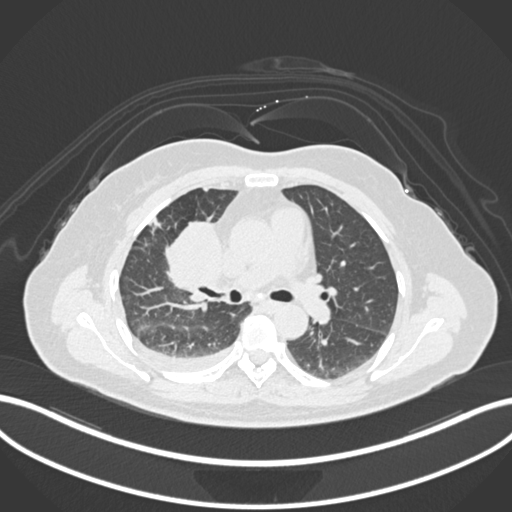
Chest CT, one axial slice. Slice 86 of 172 in the series (ordered by position). Reconstruction kernel B30f. 120 kVp. Lung window (W 1500 / L -600 HU). 1 mm slice thickness. 512 × 512 image matrix, field of view 400 × 400 mm. Patient: female, 52 years. From the clinical record (not read from this slice): clinical TNM (as recorded): T3 N1 M1.
Annotated regions visible in this slice (bounding box drawn by a radiologist):
- lung tumour (recorded histology: adenocarcinoma): bounding box (x1, y1, x2, y2) in pixels: (165, 214, 223, 299)